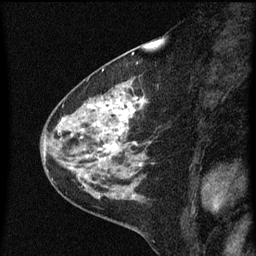
Breast MRI (dynamic contrast-enhanced), one sagittal slice; position 22 of 60 along the scan axis; dynamic contrast-enhanced series, image 2 of 3 at this slice position (ordered by acquisition); 1.5 T; TE 4.2 ms, TR 8 ms; 2 mm slice thickness; 256 × 256 image matrix, field of view 180 × 180 mm. Female patient, age 60 years.
Annotated regions visible in this slice (semi-automatically segmented with operator editing):
- analysis volume of interest (the breast-tissue region the enhancement analysis was run in; not a lesion): bounding box (x1, y1, x2, y2) in pixels: (48, 82, 154, 183)
- tumour enhancement mask (voxels above the 70 % enhancement threshold inside the analysis volume of interest): (62, 86, 145, 165)